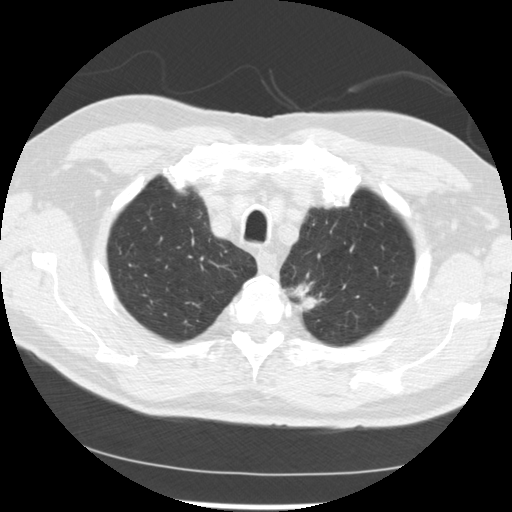
Low-dose screening chest CT, one axial slice; position 210 of 249 along the scan axis; reconstruction kernel STANDARD; lung window (W 1500 / L -600 HU); 512 × 512 image matrix.
Outlined on this slice (outlined manually by an expert reader):
- lesion 2 (tumor, upper lobe of left lung): bounding box [x1, y1, x2, y2] px = [289, 283, 322, 311]